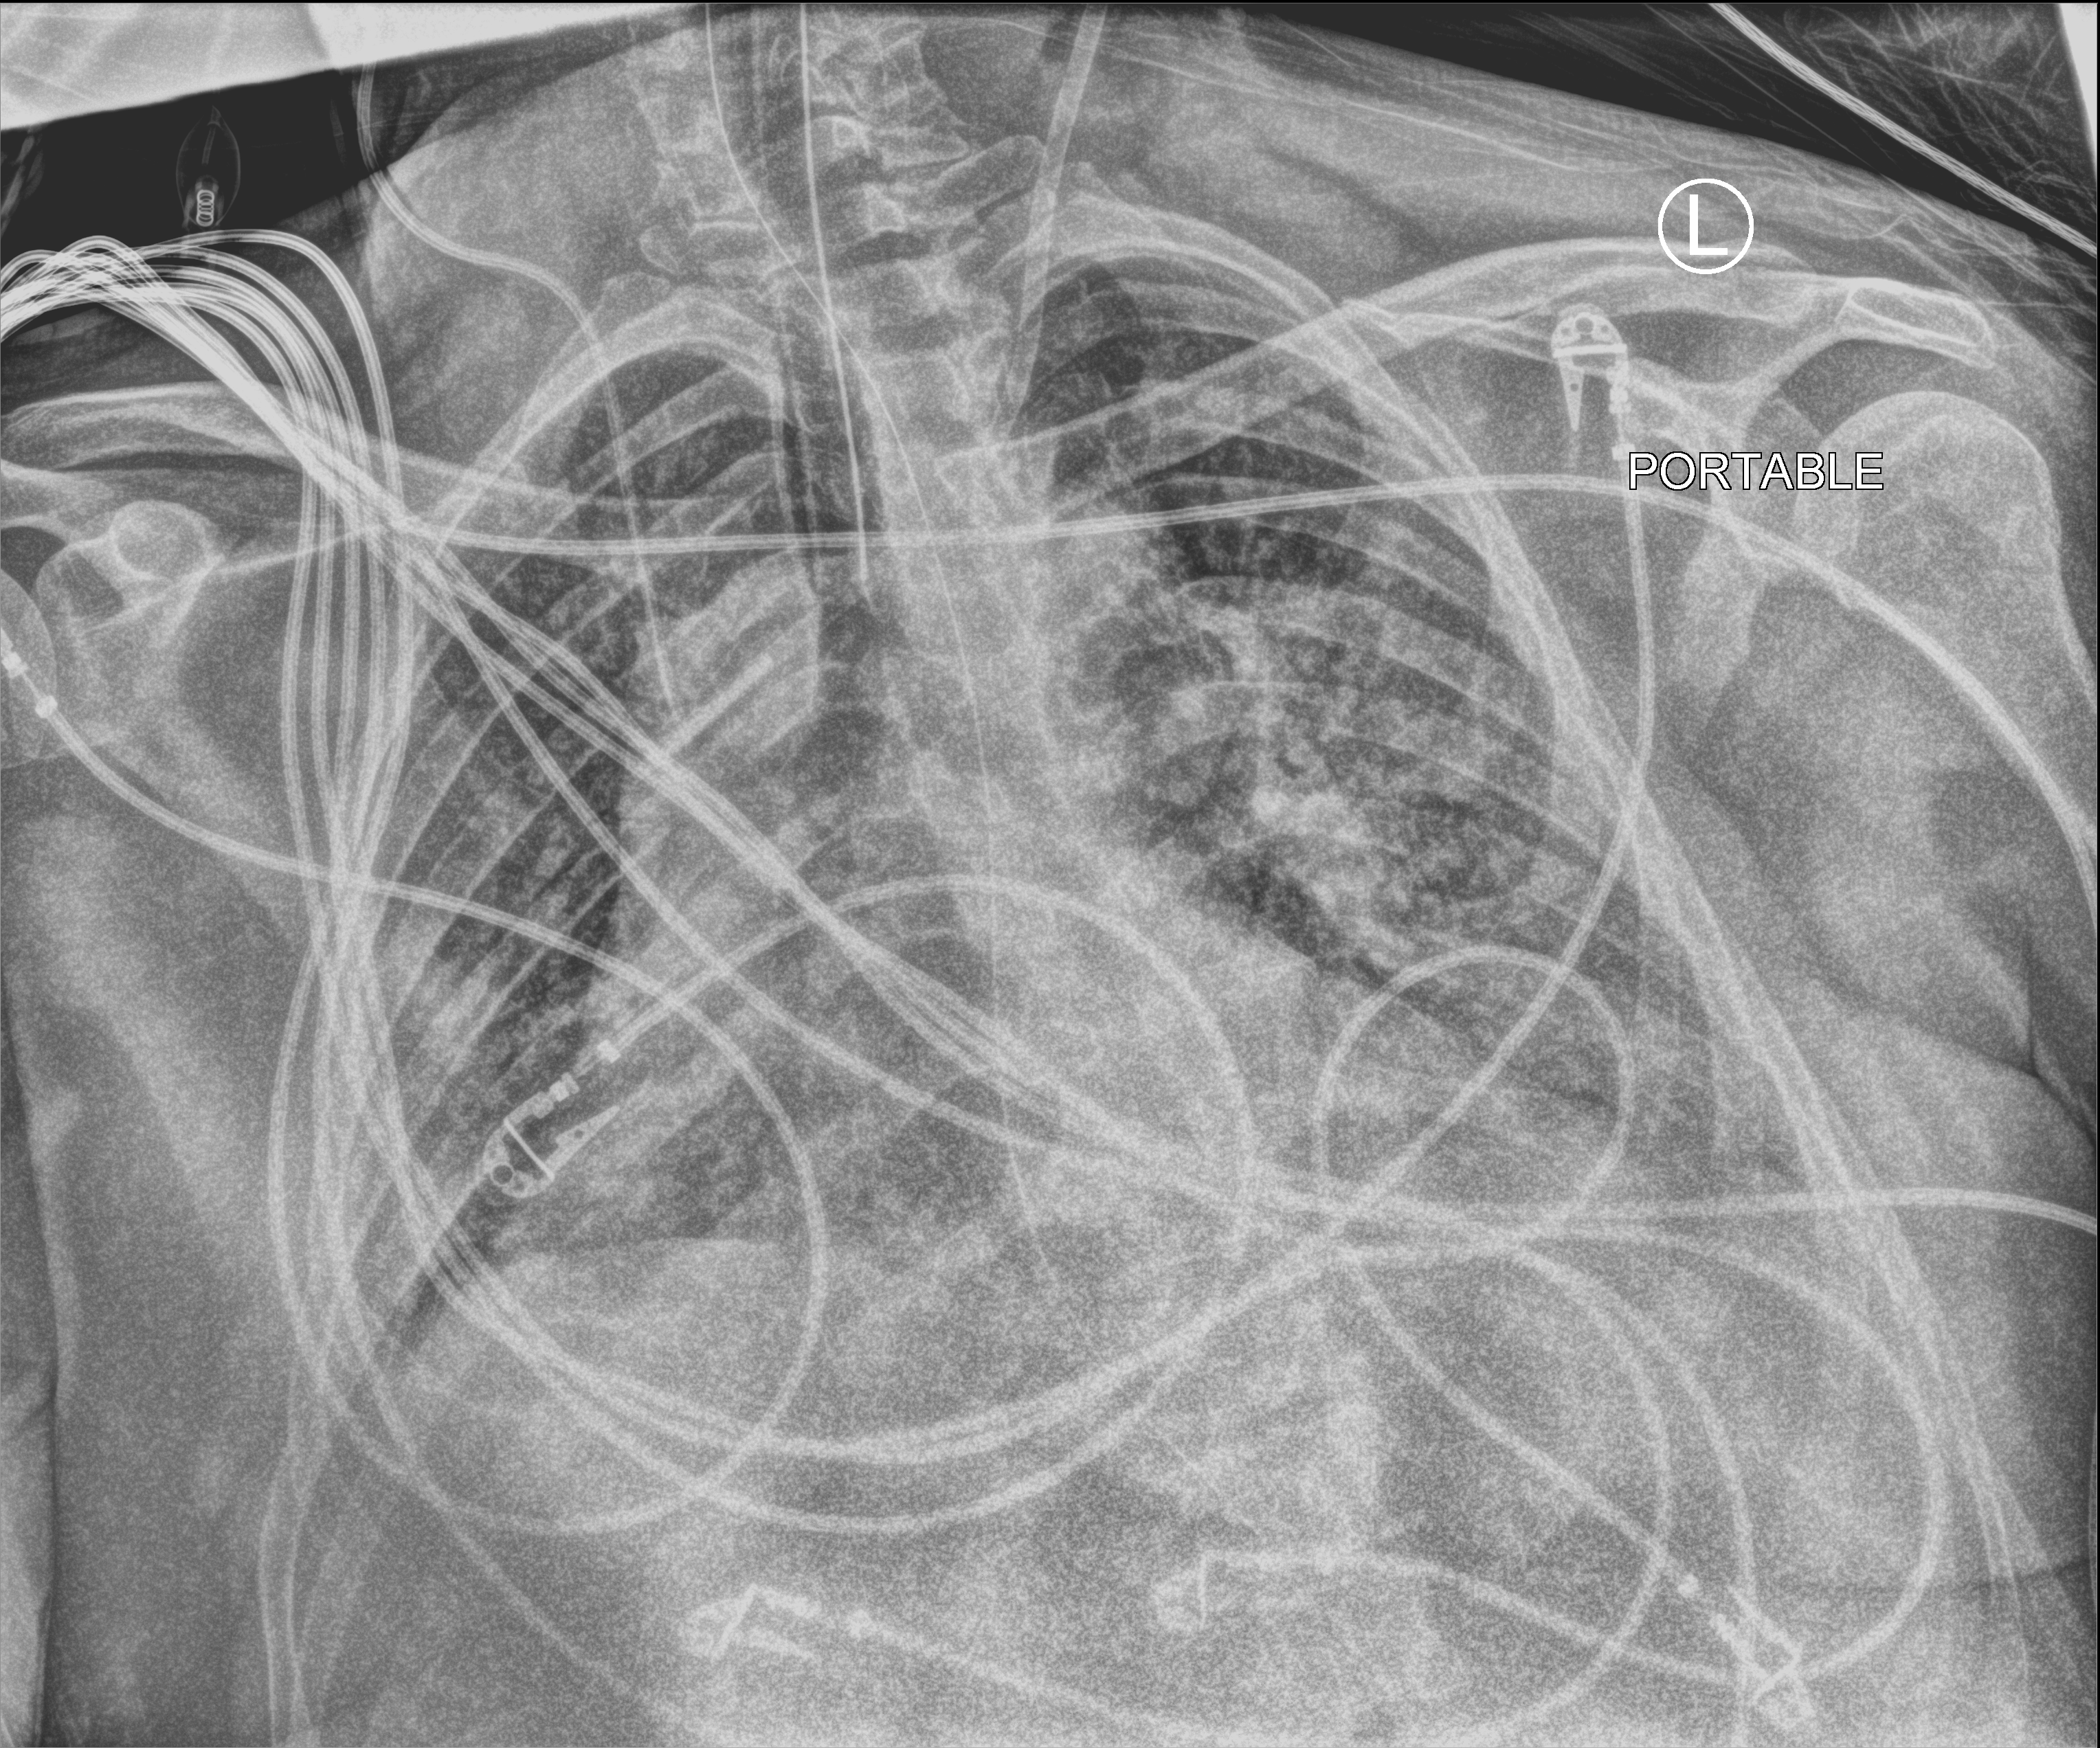
Bedside chest radiograph (computed radiography). Patient hospitalised with COVID-19; male, aged 18–59 years.
From the hospital-stay record, not from the radiograph (when in the stay this image was taken is not recorded): mechanically ventilated during this hospital stay: yes.